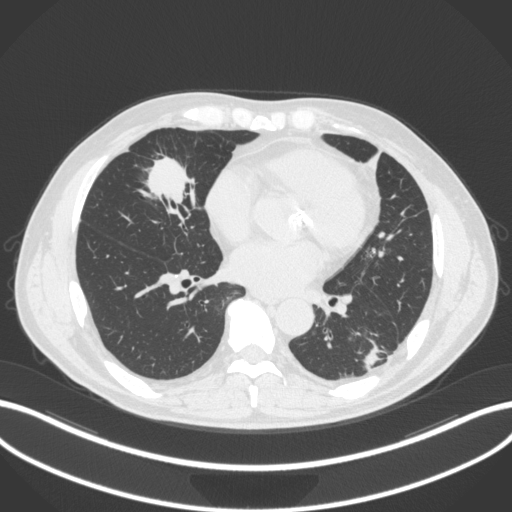
Chest CT, one axial slice. Slice 122 of 399 in the series (ordered by position). Reconstruction kernel B31f. Lung window (W 1500 / L -600 HU). 1 mm slice thickness. 512 × 512 image matrix. Patient: male, 59 years. From the clinical record (not read from this slice): clinical TNM (as recorded): T2a N1 M0.
Annotated regions visible in this slice (bounding box drawn by a radiologist):
- lung tumour (recorded histology: adenocarcinoma): bounding box [x1, y1, x2, y2] px = [134, 148, 202, 220]